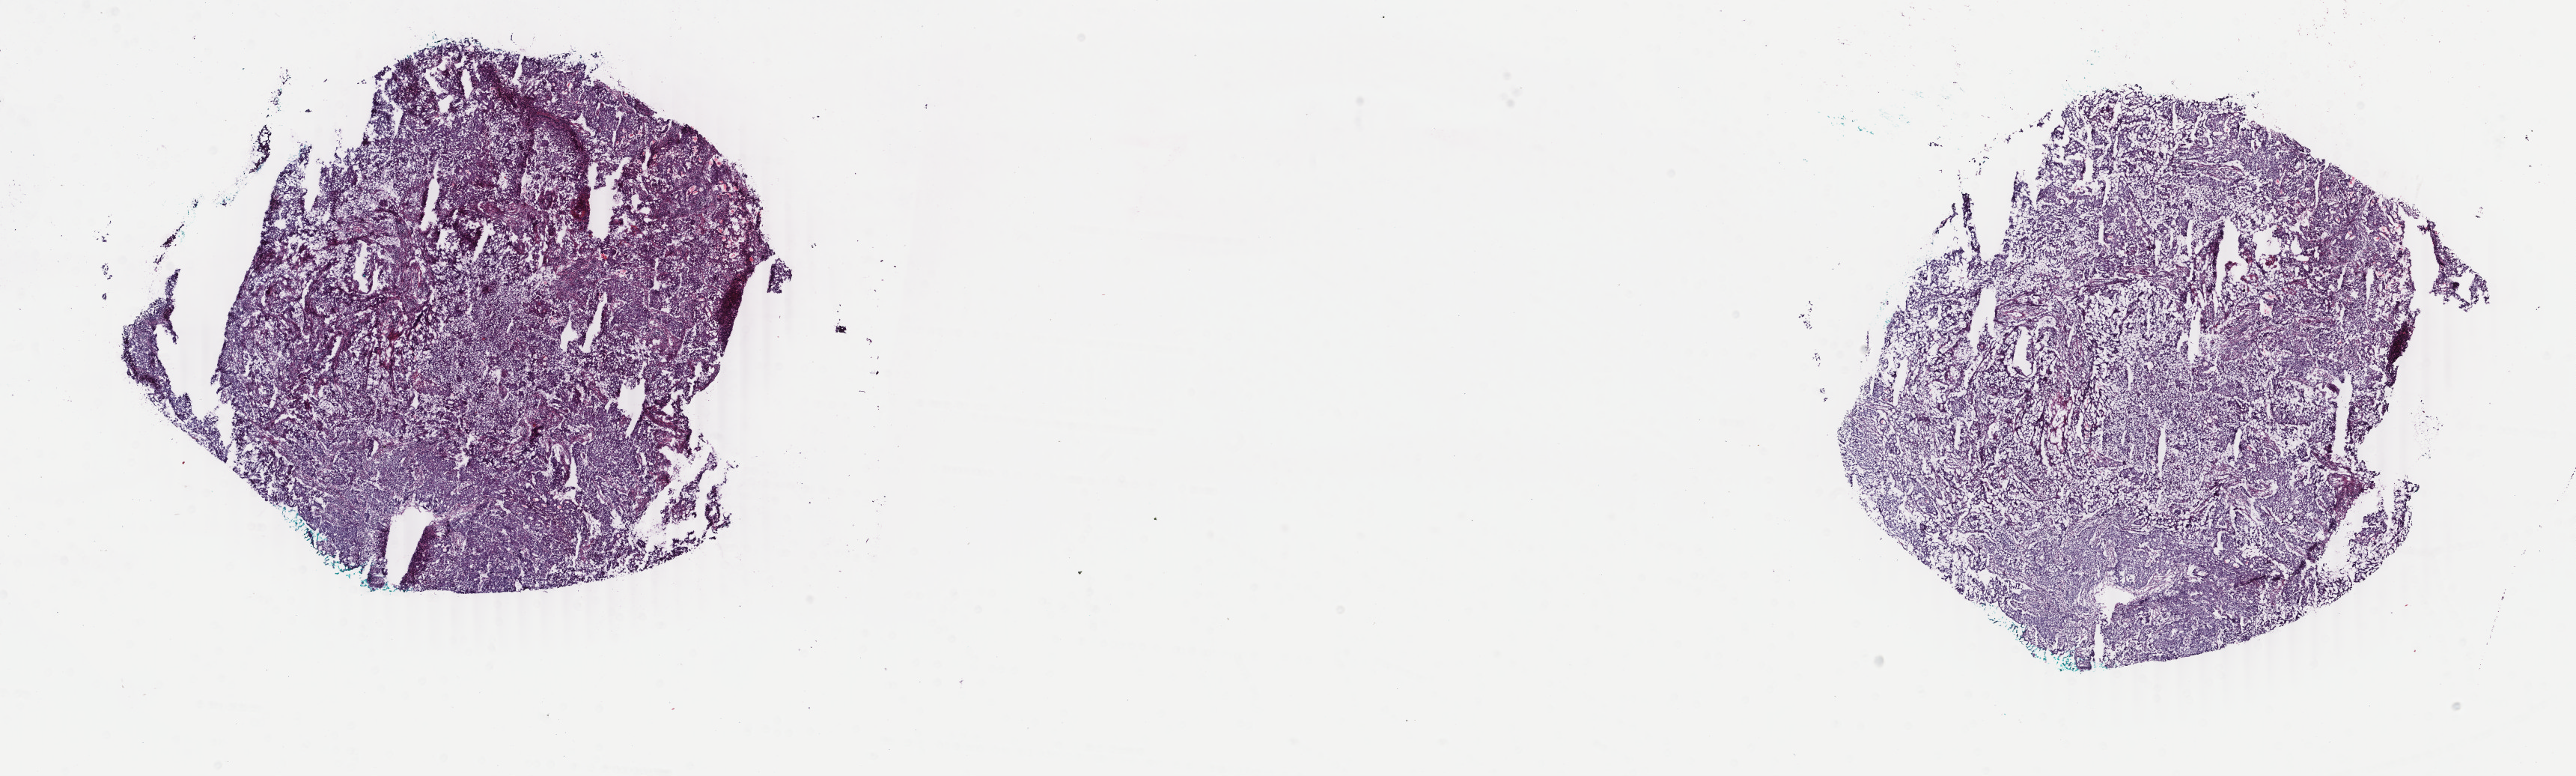
Whole-slide histology image, H&E-stained, low-resolution overview of the scanned area, about 27.4 x 8.2 mm (from a 40x scan), frozen section, sample: primary tumour, uterus. Patient: female, age at initial diagnosis 35 years. Composition of this section per pathologist review: tumour cells 80%, tumour nuclei 80%.
Histologic diagnosis: Endometrioid adenocarcinoma, NOS (corpus uteri).